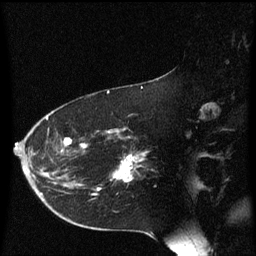
Breast MRI (dynamic contrast-enhanced), one sagittal slice. Position 38 of 60 along the scan axis. Dynamic contrast-enhanced series, image 2 of 3 at this slice position (ordered by acquisition). 1.5 T. TE 4.2 ms, TR 8.4 ms. 2 mm slice thickness. 256 × 256 image matrix, field of view 200 × 200 mm. Female patient, age 54 years. Case-level facts recorded for this patient, not image findings: setting: breast cancer imaged before/during neoadjuvant chemotherapy; receptor status: HR-positive, HER2-negative.
Structures marked on this image (semi-automatic segmentation, software-assisted and operator-edited):
- analysis volume of interest (the breast-tissue region the enhancement analysis was run in; not a lesion): bounding box (x1, y1, x2, y2) in pixels: (102, 130, 147, 191)
- tumour enhancement mask (voxels above the 70 % enhancement threshold inside the analysis volume of interest): (115, 156, 144, 183)